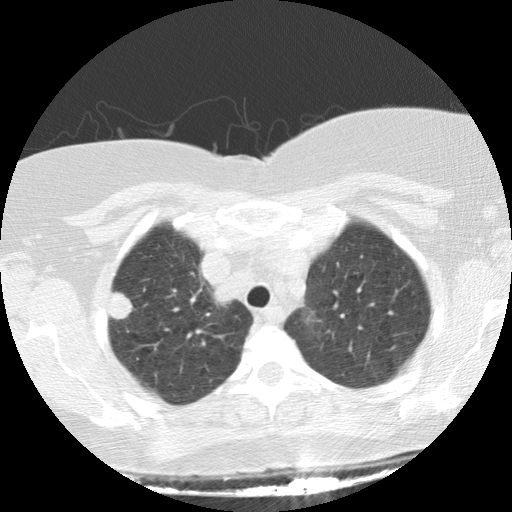
Low-dose screening chest CT, one axial slice. Position 112 of 136 along the scan axis. Reconstruction kernel STANDARD. 120 kVp. Lung window (W 1500 / L -600 HU). 2.5 mm slice thickness. 512 × 512 image matrix, field of view 330 × 330 mm.
Structures marked on this image (outlined manually by an expert reader):
- lesion 1 (tumor, upper lobe of right lung): bounding box [x1, y1, x2, y2] px = [109, 290, 133, 320]